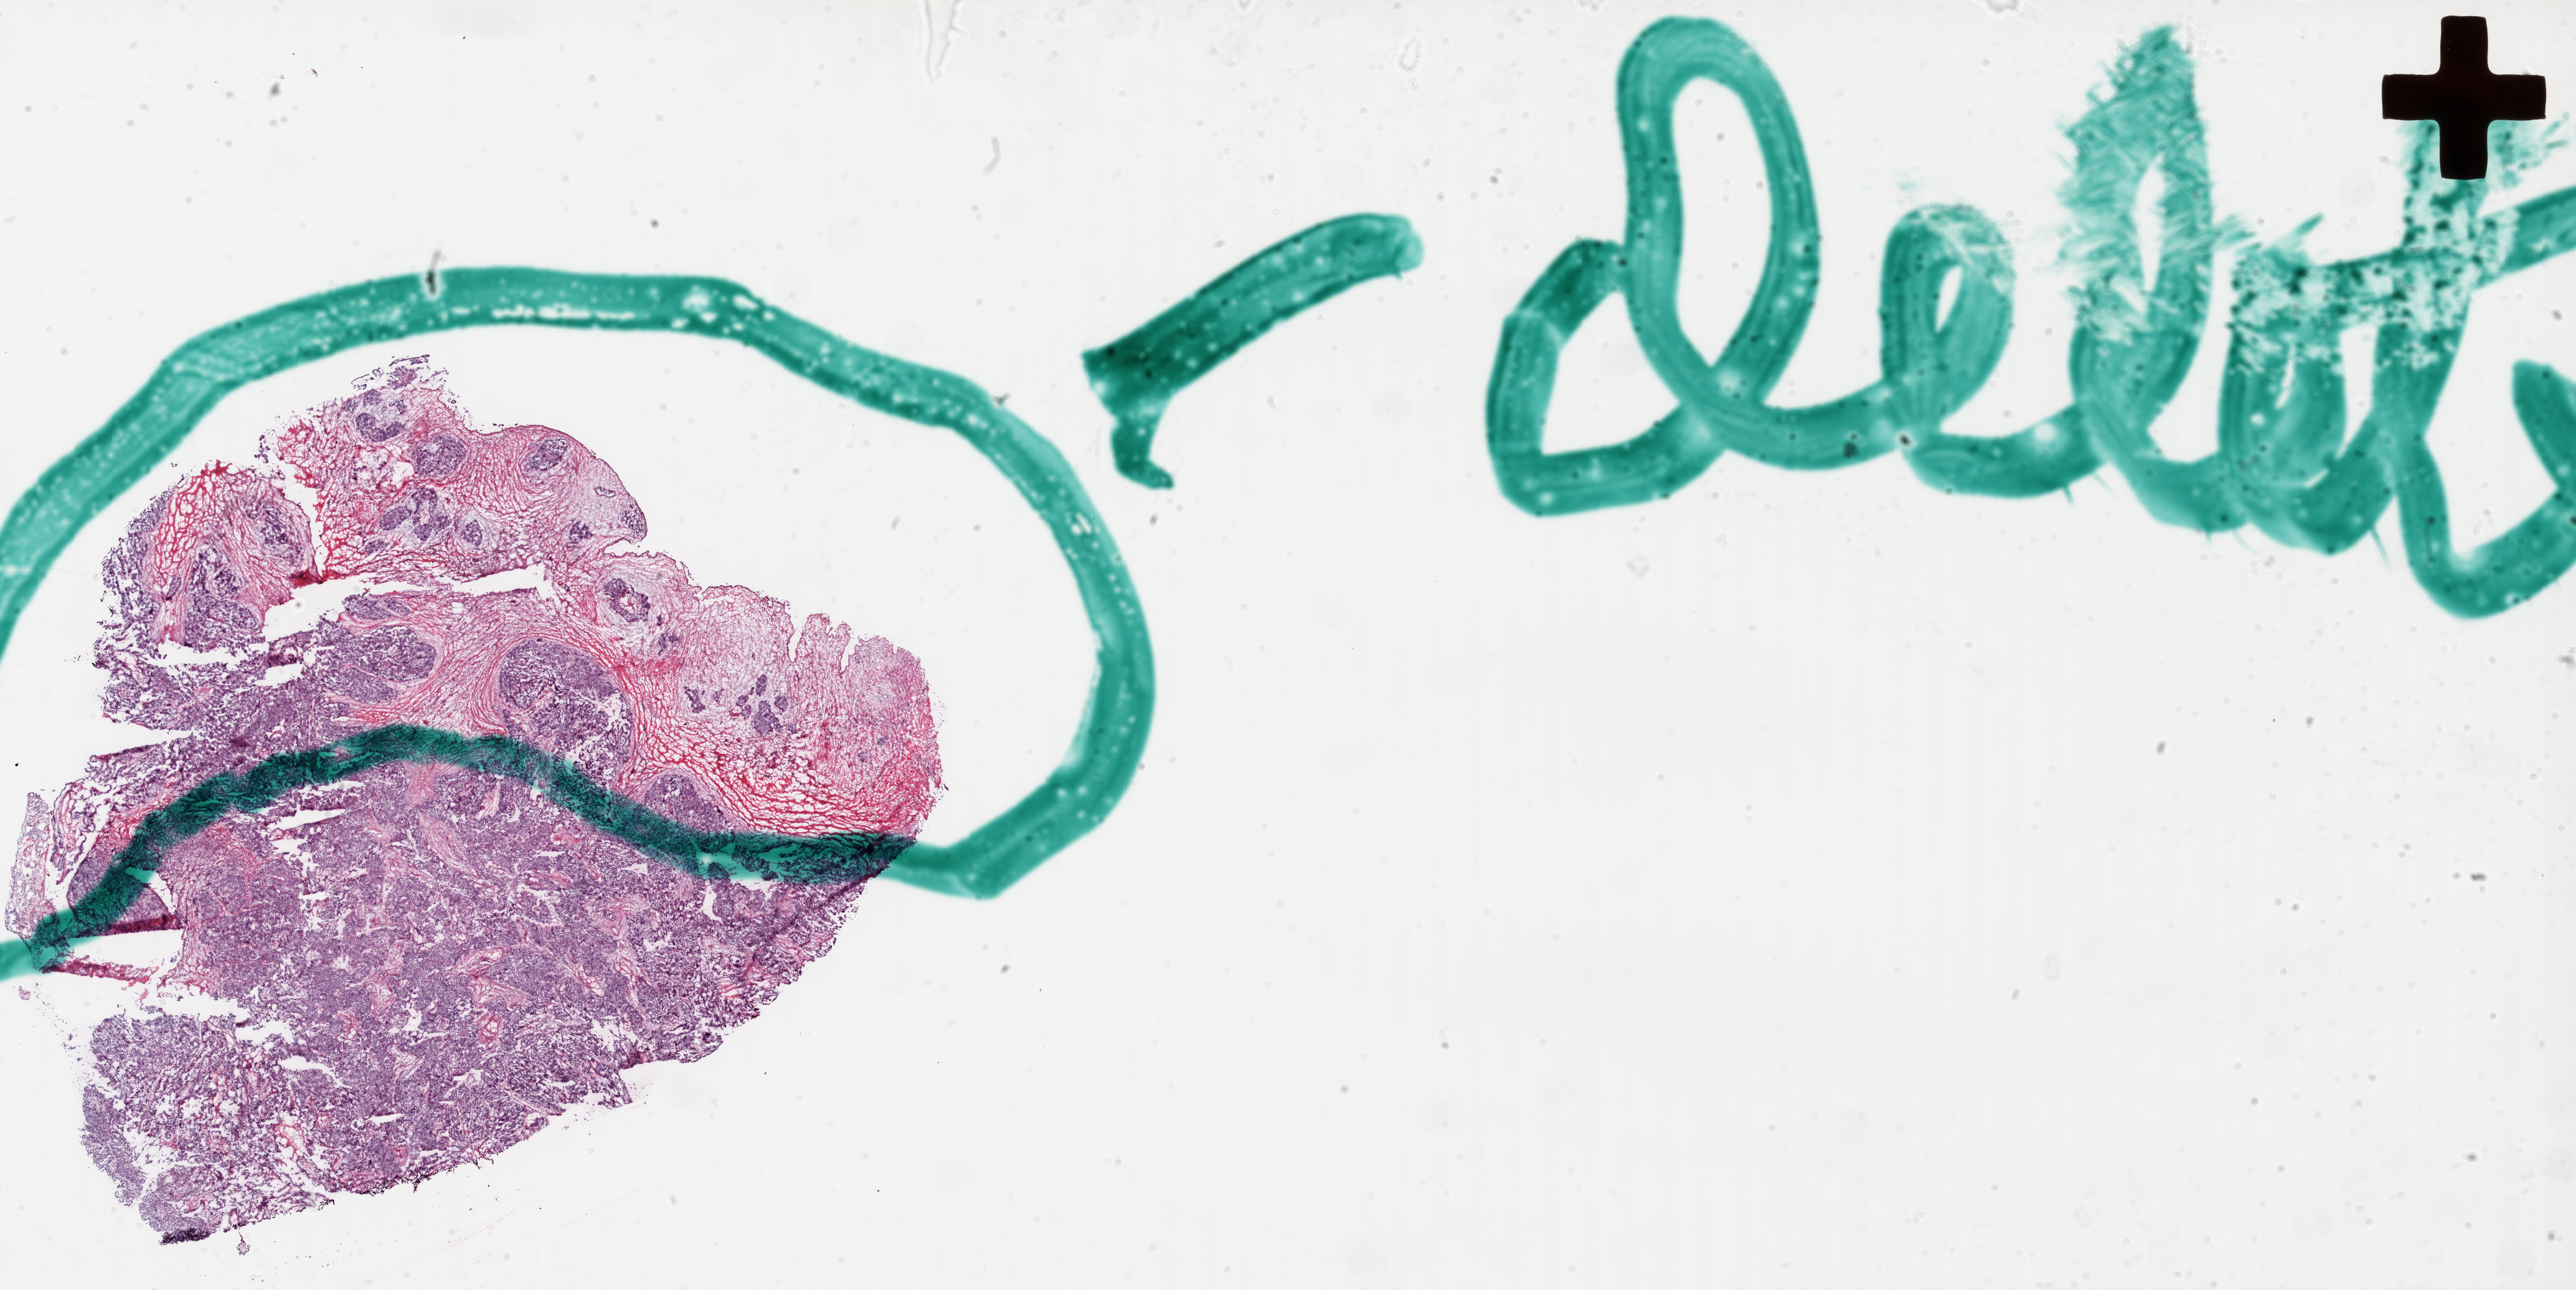
Digitized H&E-stained tissue section (whole slide), whole scanned area (about 33.4 x 16.7 mm) shown as a low-resolution overview; frozen section from the top of the tissue portion; sample: primary tumour, ovary. Patient: female, age at initial diagnosis 75 years. Histologic grade: G3 (poorly differentiated). Composition of this section per pathologist review: tumour cells 89%, tumour nuclei 90%, normal cells 10%, necrosis 1%.
- FIGO stage: IV
- histologic diagnosis: Serous cystadenocarcinoma, NOS